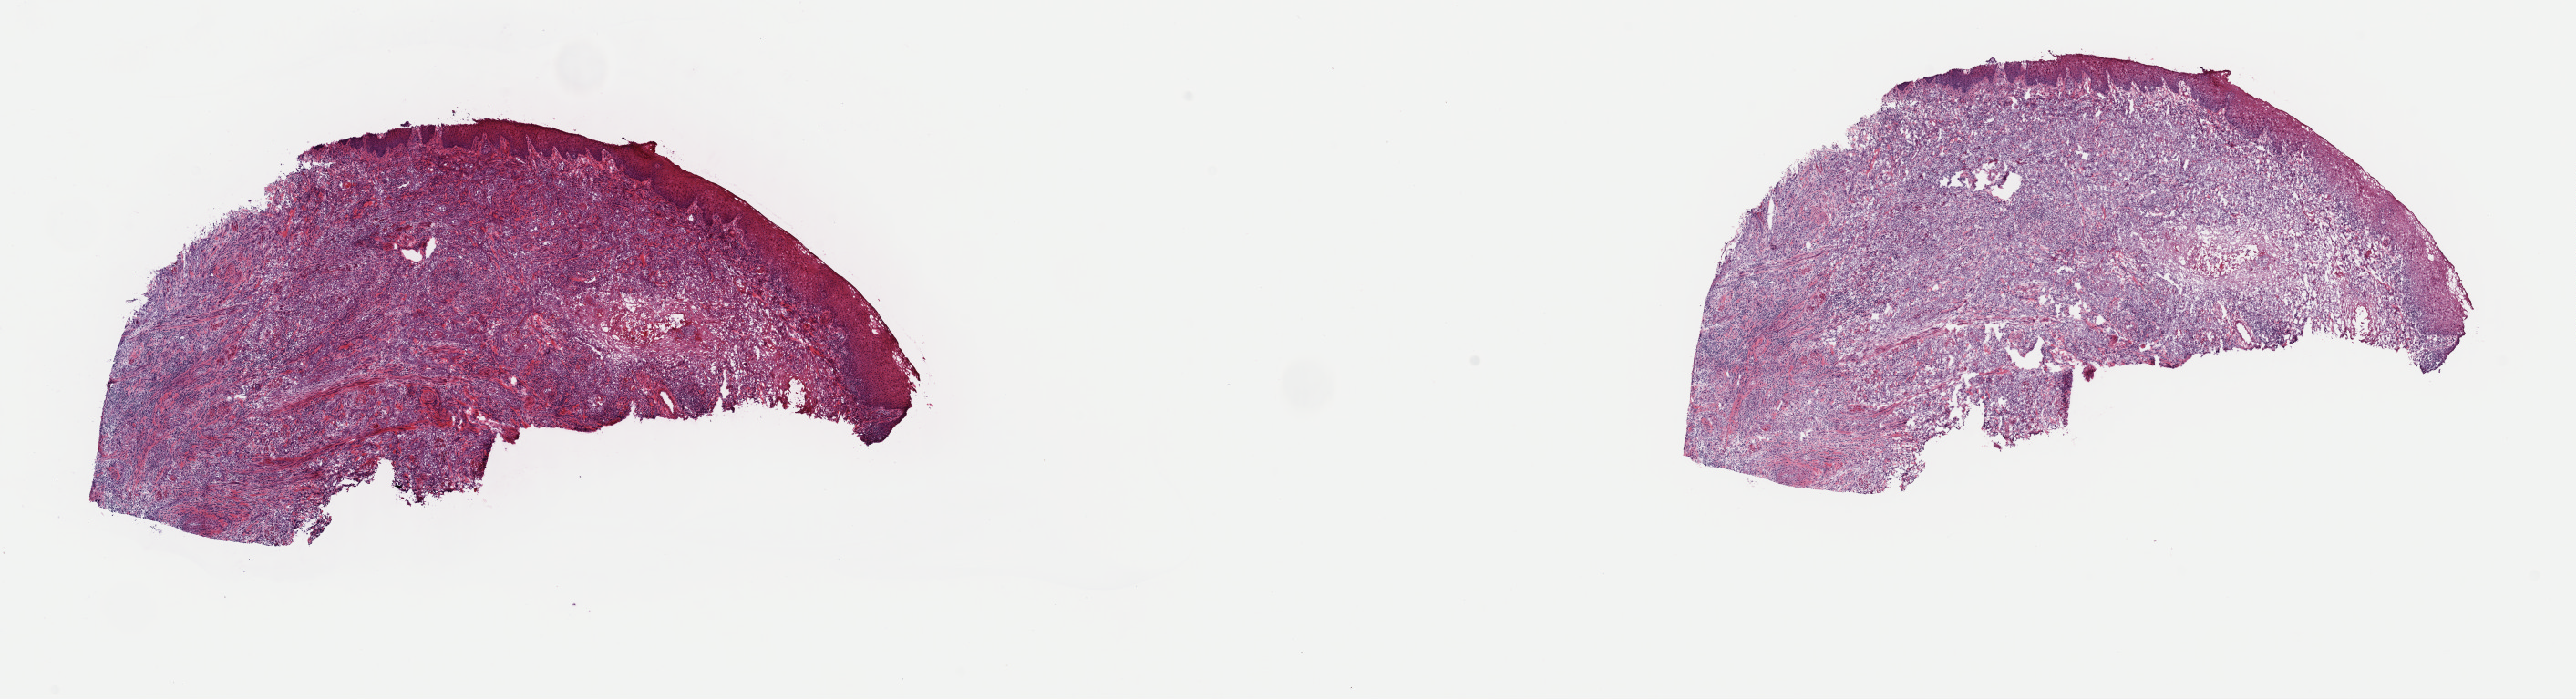
H&E-stained whole-slide image — low-resolution overview of the scanned area, about 22.3 x 6.1 mm (acquisition: 40x scan), frozen section from the top of the tissue portion, head and neck, primary tumour sample. Patient: male, age at initial diagnosis 58 years. Histologic grade: G3 (poorly differentiated). Composition of this section per pathologist review: tumour cells 70%, tumour nuclei 70%, normal cells 10%, stromal cells 20%, necrosis 0%. Inflammatory infiltration, as recorded: lymphocyte infiltration 20%, monocyte infiltration 0%, neutrophil infiltration 0%.
Laterality: right. AJCC pathologic stage: I (7th edition). Histologic diagnosis: Squamous cell carcinoma, NOS (tongue, NOS).